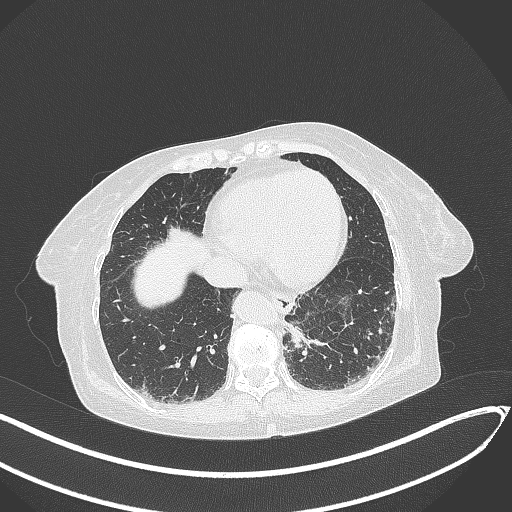
Chest CT, one axial slice. Position 55 of 324 along the scan axis. Reconstruction kernel B70f. 120 kVp. Lung window (W 1500 / L -600 HU). 512 × 512 image matrix. Female patient, age 82 years. Case-level facts recorded for this patient, not image findings: clinical TNM (as recorded): T1b N0 M1.
Annotated regions visible in this slice (rectangle marked by the reading radiologist):
- lung tumour (recorded histology: adenocarcinoma): bounding box <283,323,330,364> (left, top, right, bottom; pixels)